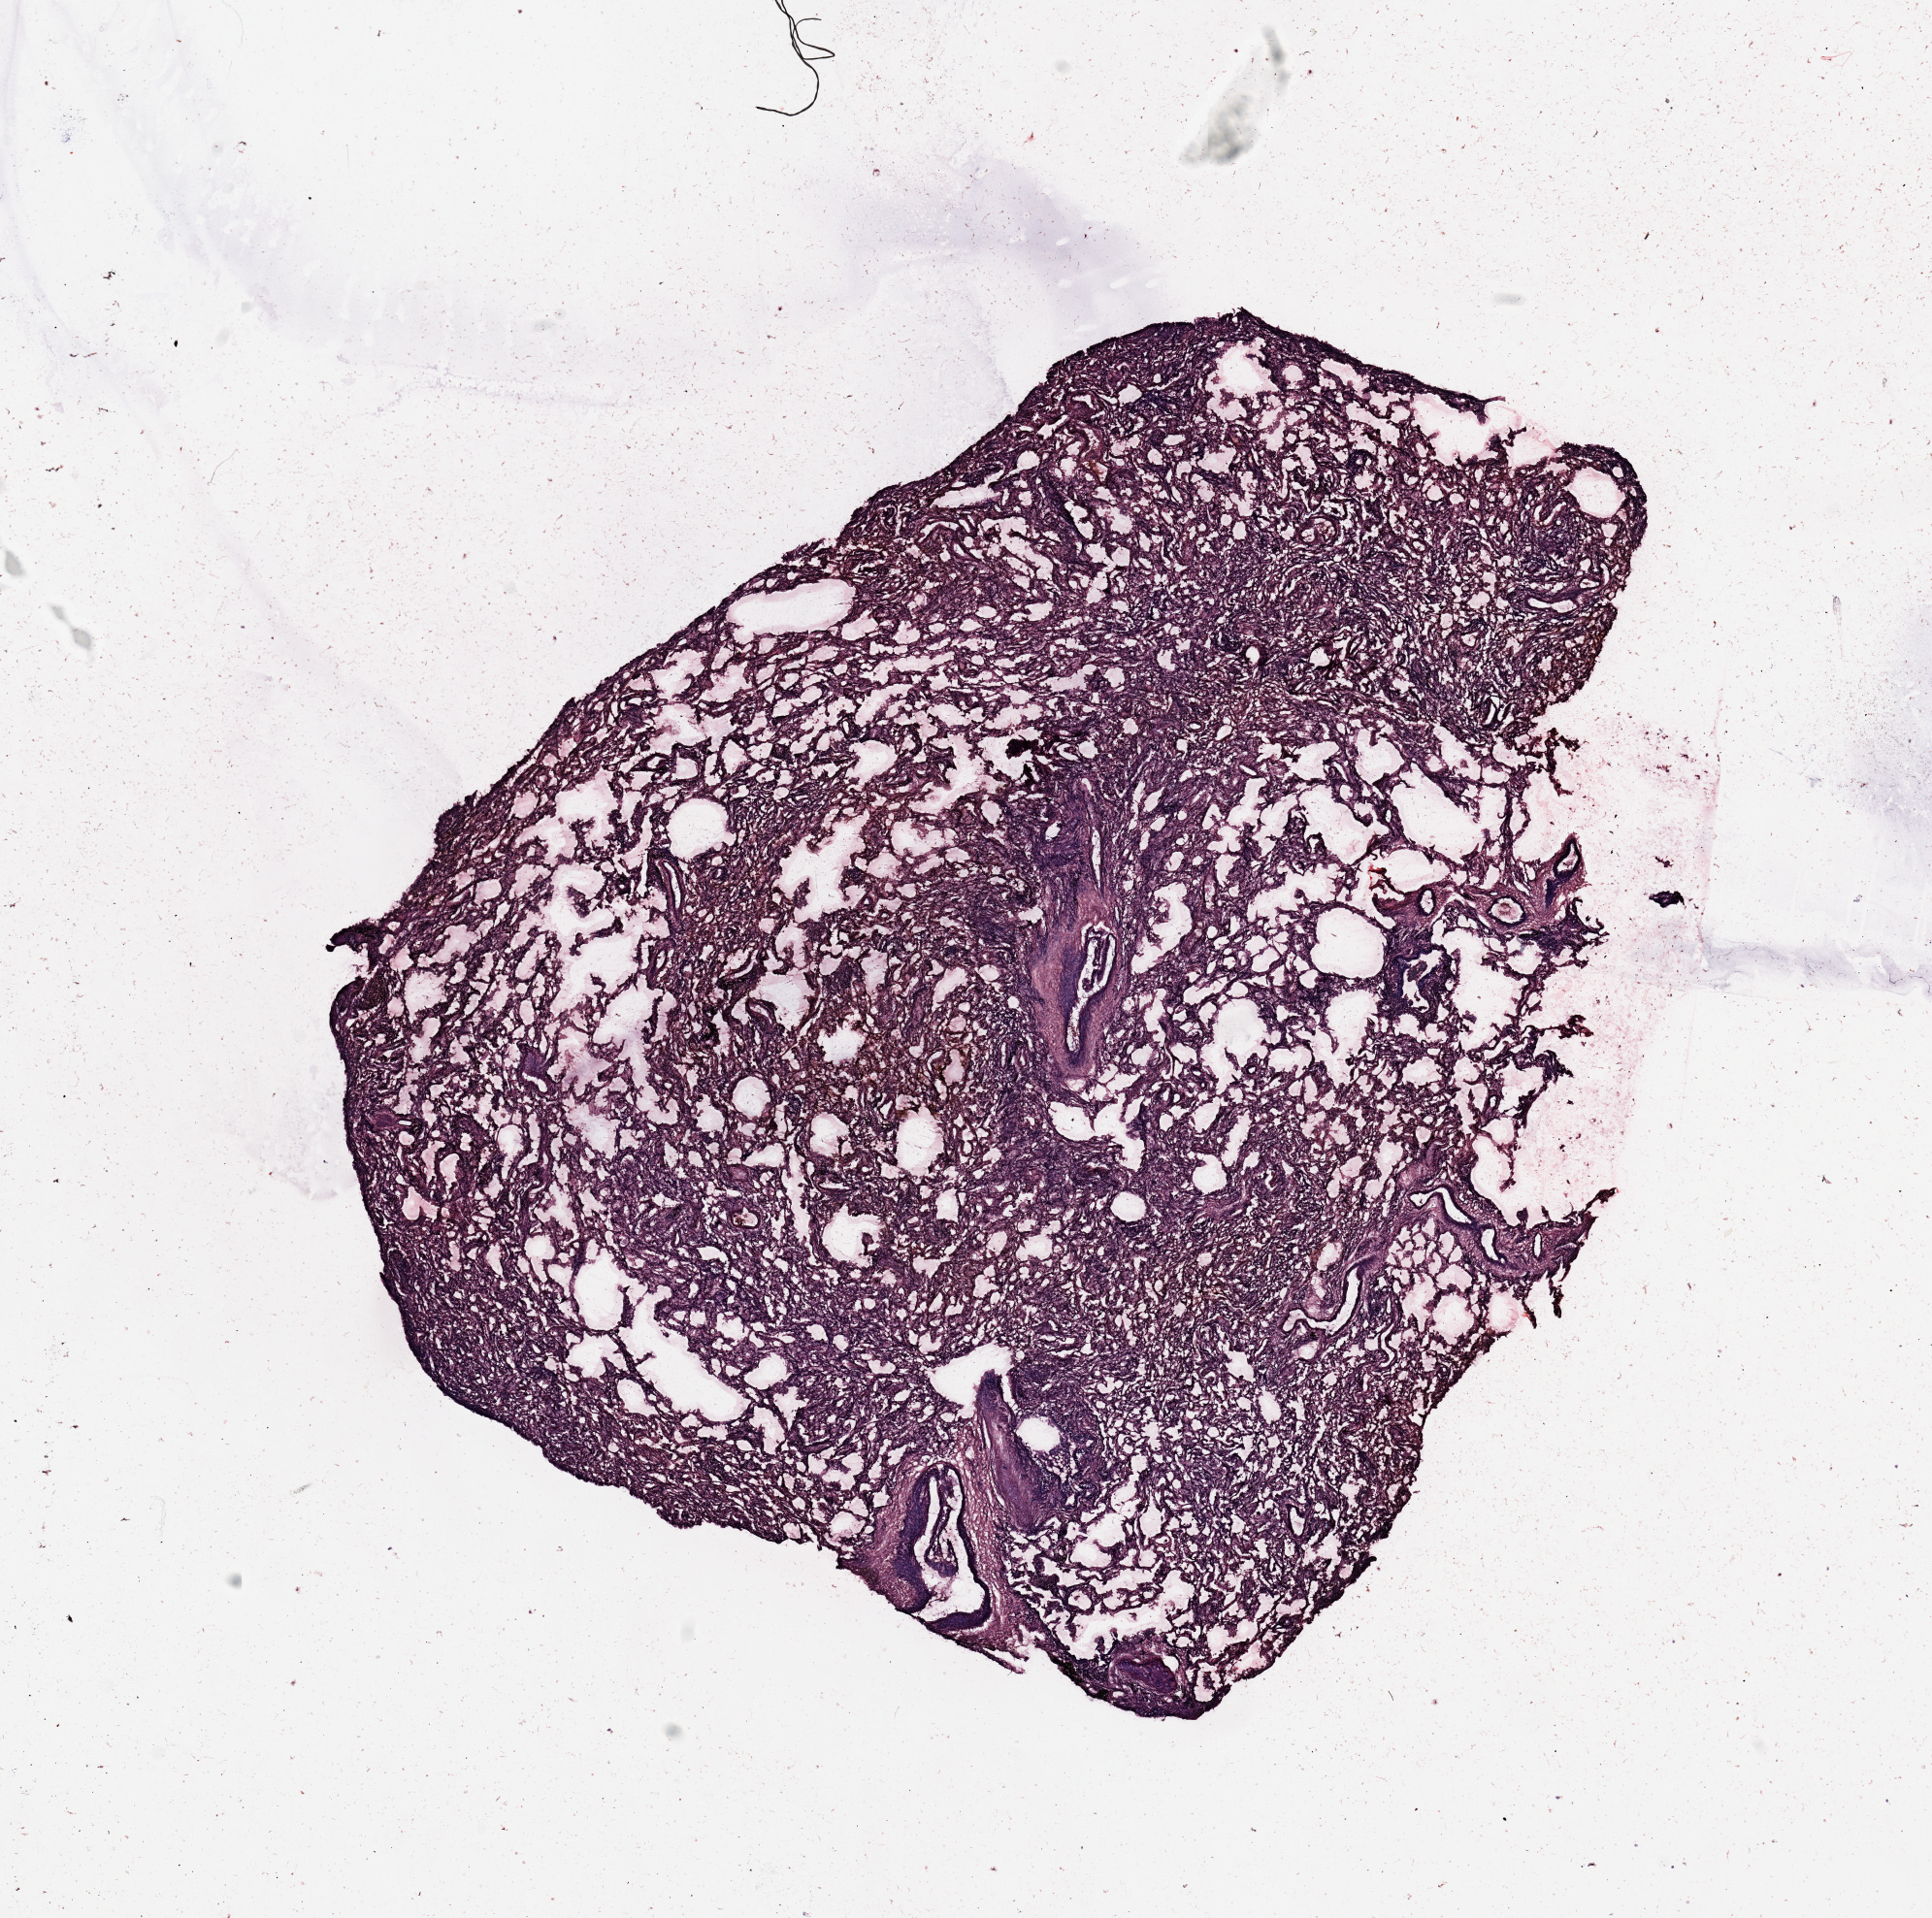
Digitized Hematoxylin and eosin (H&E) stained tissue section (whole slide), a low-resolution overview of the entire scanned area, about 15.8 x 15.6 mm, normal (non-tumour) tissue sample, sampled site: lung. Patient: male, age 57 years.
This section: normal (non-tumour) tissue from the same patient. Patient diagnosis: Adenocarcinoma, NOS.